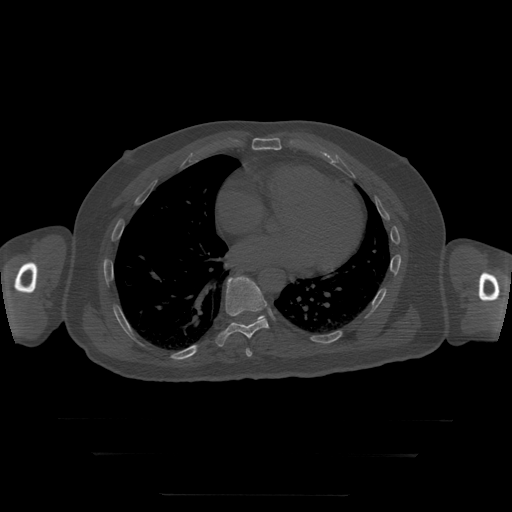
CT including the spine, one axial slice; slice 143 of 397 in the series (ordered by position); bone window (W 1800 / L 400 HU); 512 × 512 image matrix, field of view 510 × 510 mm. Patient age 73 years. From the clinical record (not read from this slice): primary cancer: prostate.
Annotated regions visible in this slice (semi-automatically segmented with operator editing):
- T10 vertebra: bounding box <236,315,265,320> (left, top, right, bottom; pixels)
- T8 vertebra: <246,349,252,357>
- T9 vertebra: <216,276,269,347>